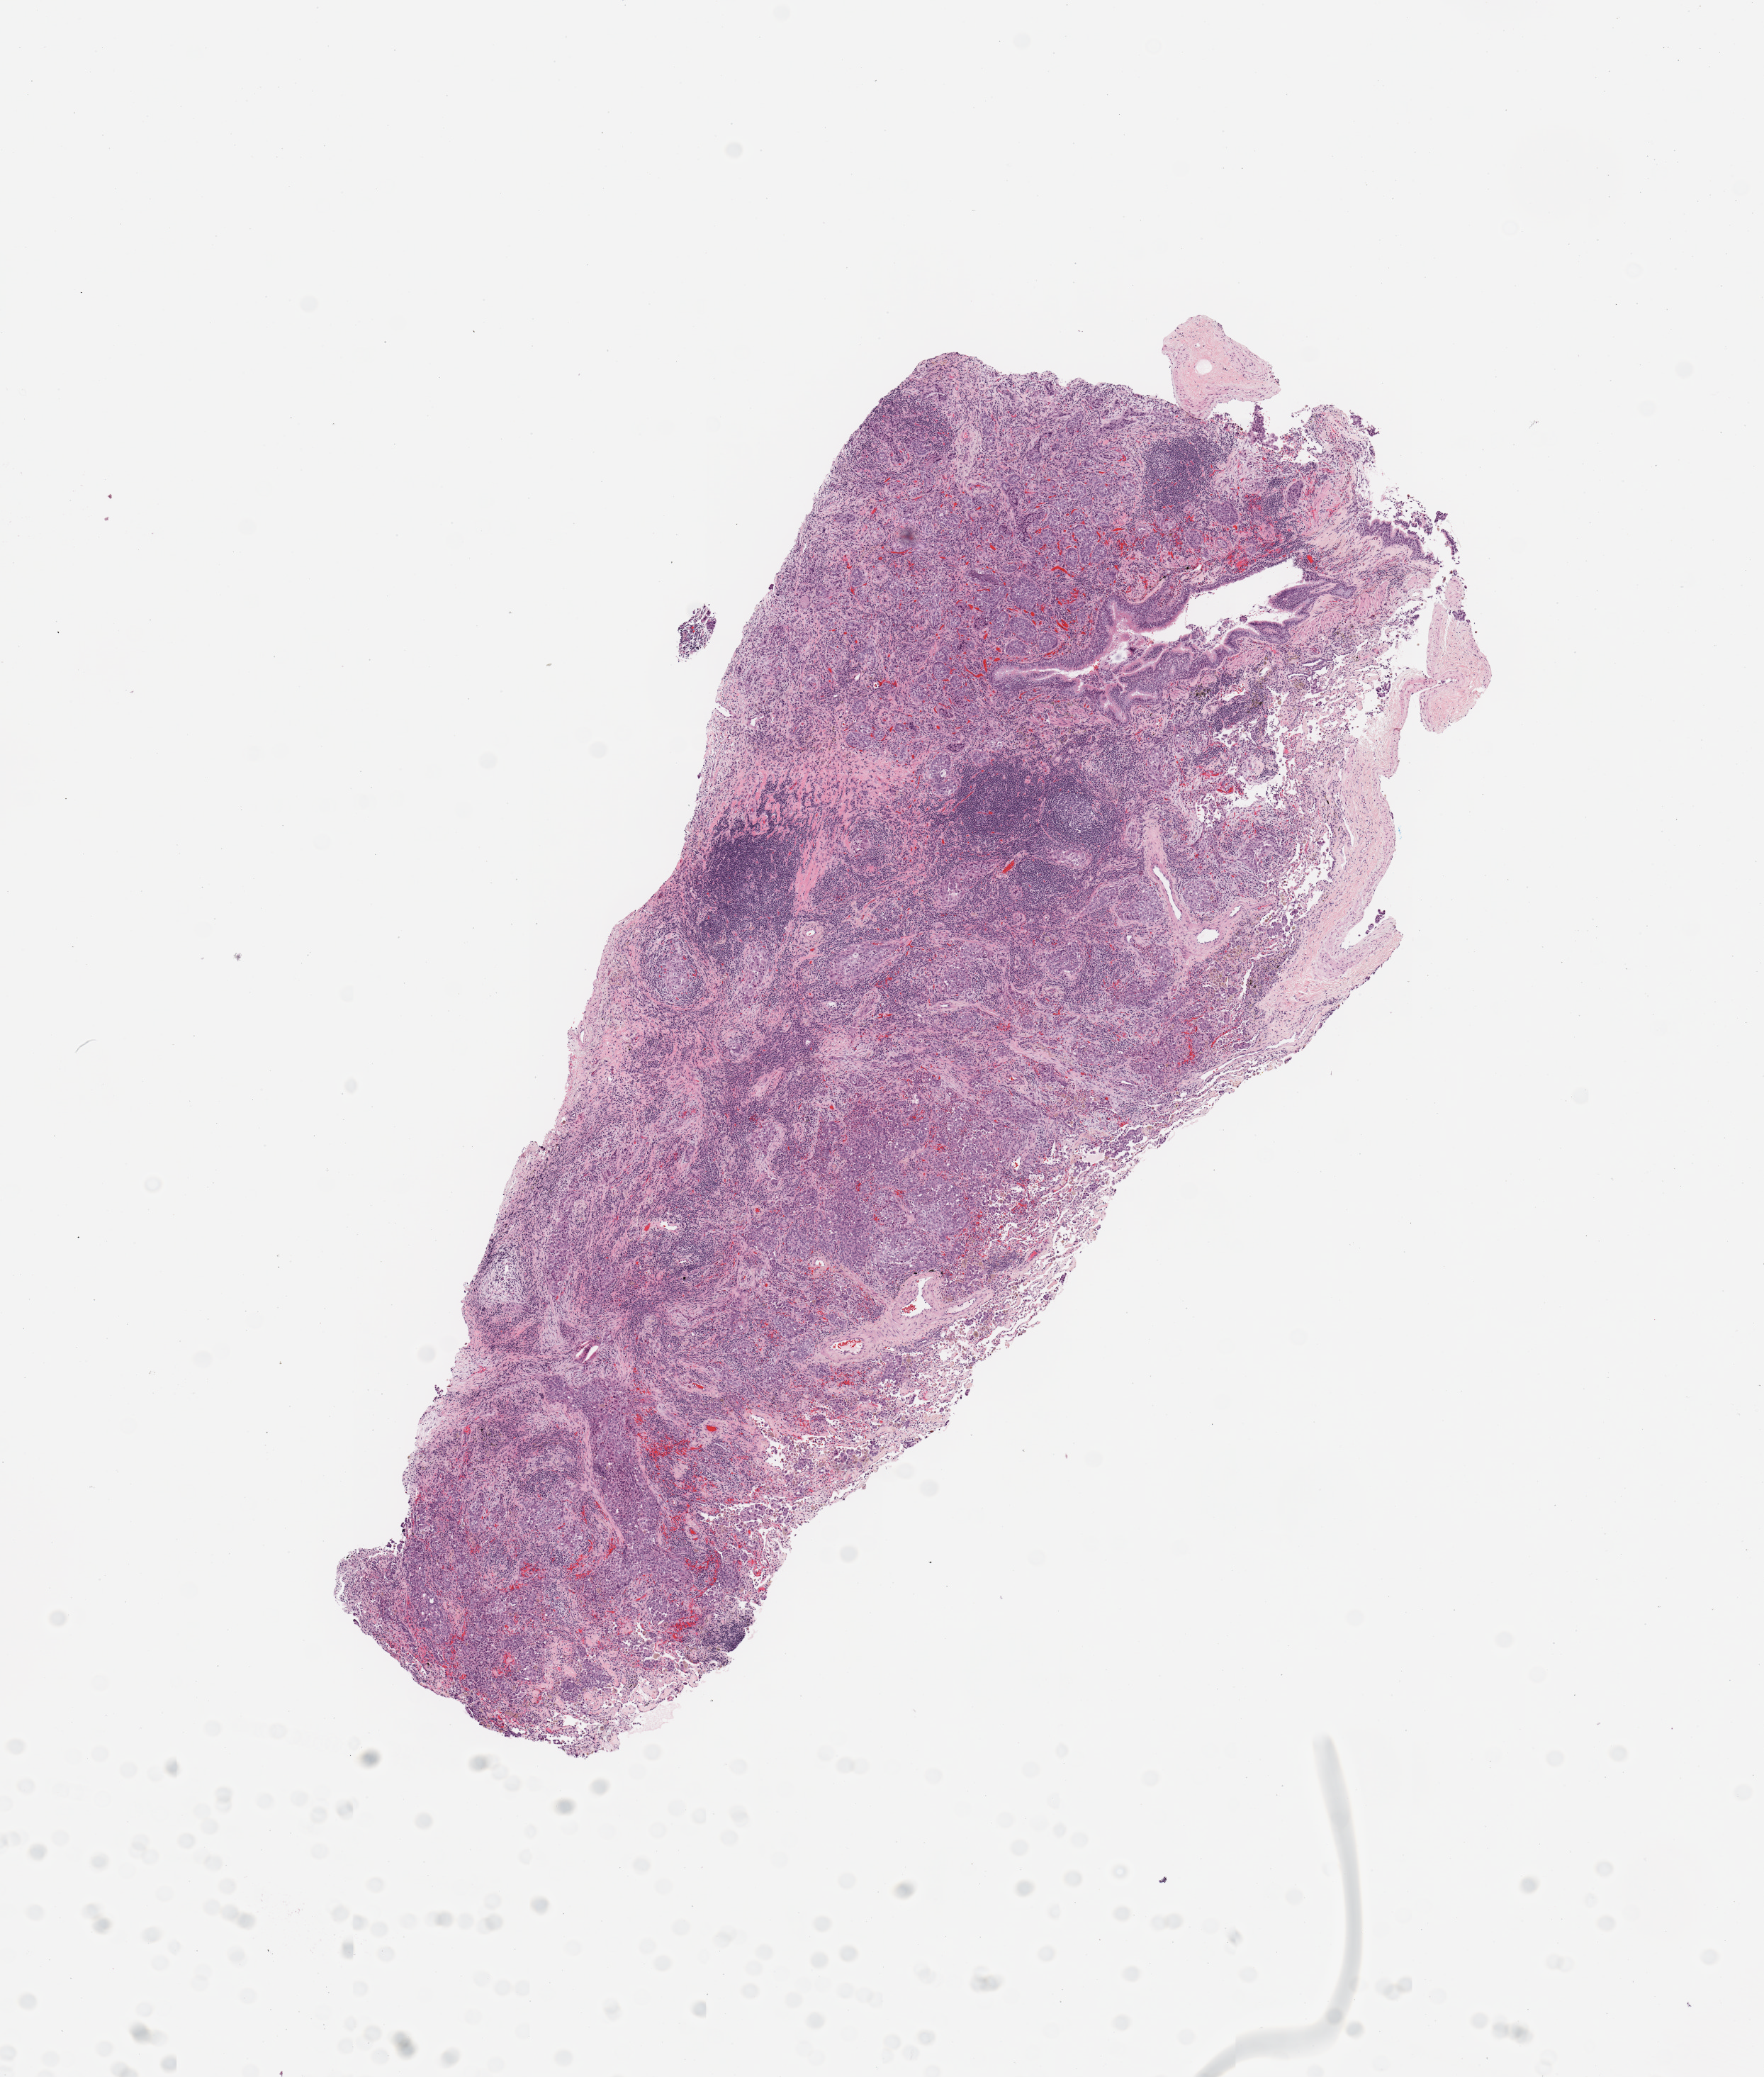
Whole-slide histology image, H&E — shown as a low-resolution overview of the whole scanned area (about 9.8 x 11.6 mm, from a 20x scan), tumour tissue sample, sampled site: lung. Patient: male, age 62 years. Histologic grade: G2 (moderately differentiated). Slide review estimates, as recorded: tumour nuclei 70%, necrosis 0%.
* diagnosis: Adenocarcinoma, NOS
* AJCC pathologic stage: IA
* primary tumour site (as recorded): left upper lobe